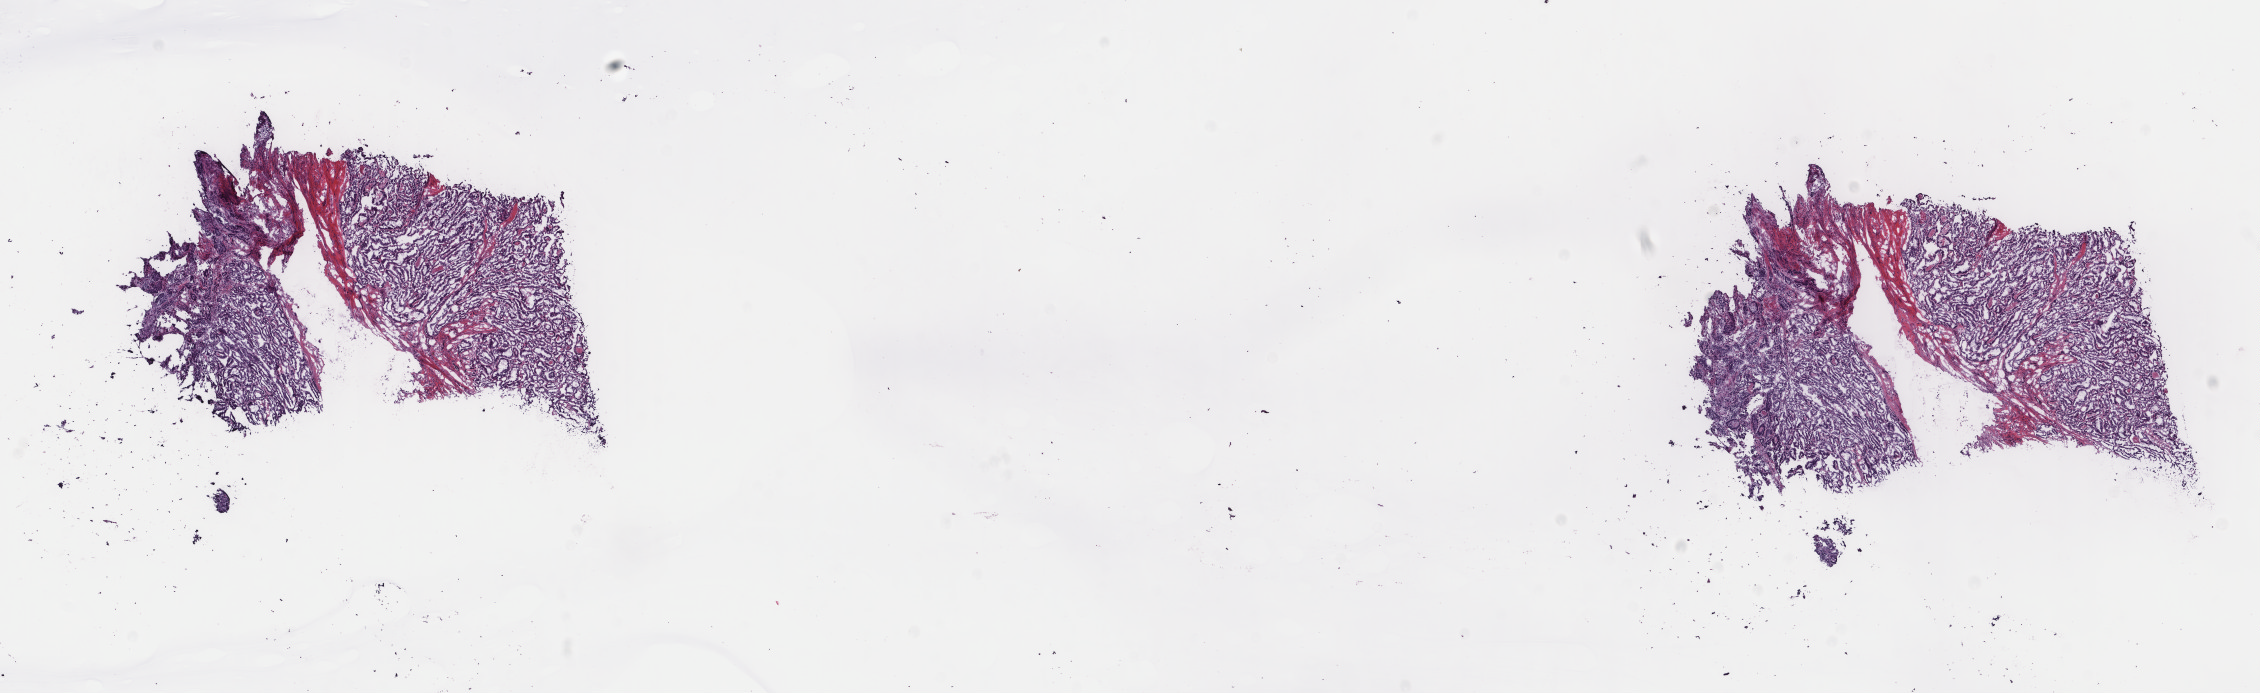
Whole-slide histology image, H&E-stained, whole scanned area (about 17.9 x 5.5 mm, acquisition: 40x scan) shown as a low-resolution overview; frozen section; sample: primary tumour, thyroid. Male patient; age at initial diagnosis 70 years. Slide review estimates, as recorded: tumour cells 90%, tumour nuclei 90%, normal cells 0%, stromal cells 10%, necrosis 0%. Inflammatory infiltration, as recorded: lymphocyte infiltration 0%, monocyte infiltration 0%, neutrophil infiltration 0%.
Laterality: left. Lymph nodes positive (case pathology): 3 of 3 examined. Diagnosis: Papillary carcinoma, columnar cell (thyroid gland). AJCC pathologic stage: III (7th edition).